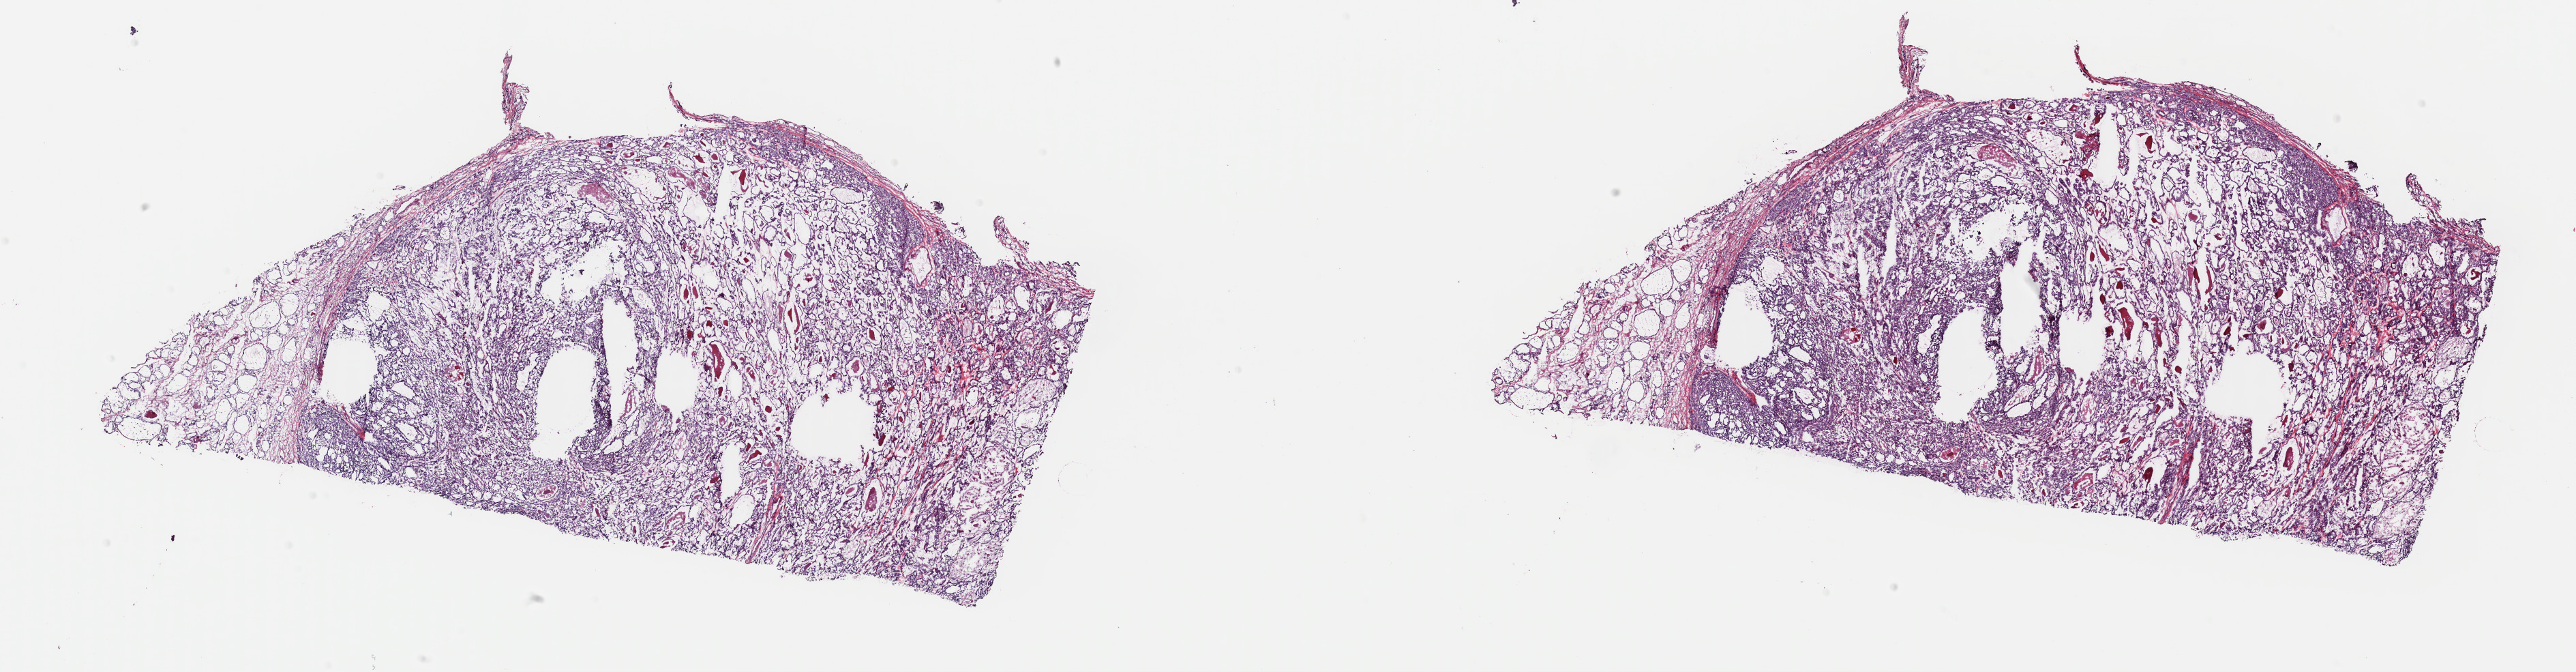
Hematoxylin and eosin (H&E) stained whole-slide image, a low-resolution overview of the entire scanned area, about 29.8 x 7.8 mm; frozen section from the top of the tissue portion; sample: primary tumour, thyroid. Patient: female, age at initial diagnosis 59 years. Pathologist review of this section (percent, as recorded): tumour cells 80%, tumour nuclei 90%, normal cells 10%, stromal cells 10%, necrosis 0%. Inflammatory infiltration, as recorded: lymphocyte infiltration 1%, monocyte infiltration 0%, neutrophil infiltration 0%.
- laterality: right
- pathologic diagnosis: Papillary adenocarcinoma, NOS
- AJCC pathologic stage: I (7th edition)